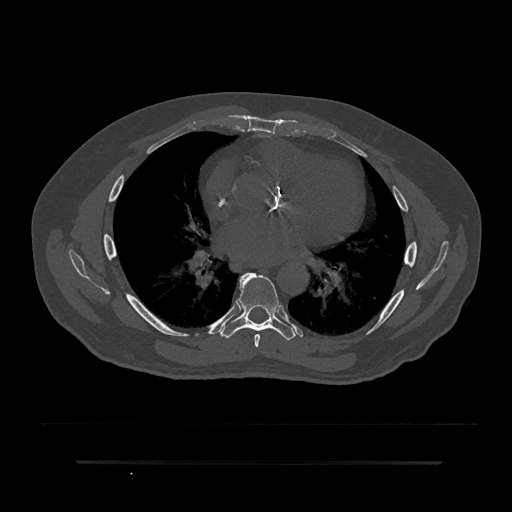
CT including the spine, one axial slice; position 491 of 797 along the scan axis; 120 kVp; bone window (W 1800 / L 400 HU); 512 × 512 image matrix, field of view 464 × 464 mm. Patient: male, 59 years. From the clinical record (not read from this slice): primary cancer: bile ducts; vertebrae with lytic lesions (as recorded): T10.
Structures marked on this image (semi-automatic segmentation, software-assisted and operator-edited):
- T6 vertebra: box from (x=254, y=334) to (x=260, y=347) px
- T7 vertebra: (x=220, y=273)–(x=296, y=340)